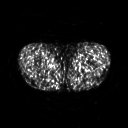
FDG PET of an extremity soft-tissue mass (from a PET/CT study), one axial slice. Slice 264 of 311 in the series (ordered by position). 3.27 mm slice thickness. 128 × 128 image matrix, field of view 500 × 500 mm. Patient: male, 29 years. From the clinical record (not read from this slice): histological type: mixoid liposarcoma; grade: low; site of the primary tumour: left thigh.
Structures marked on this image (expert contour drawn on MRI and transferred to this co-registered scan by the dataset authors):
- gross tumour volume (mass): box from (x=76, y=59) to (x=81, y=63) px